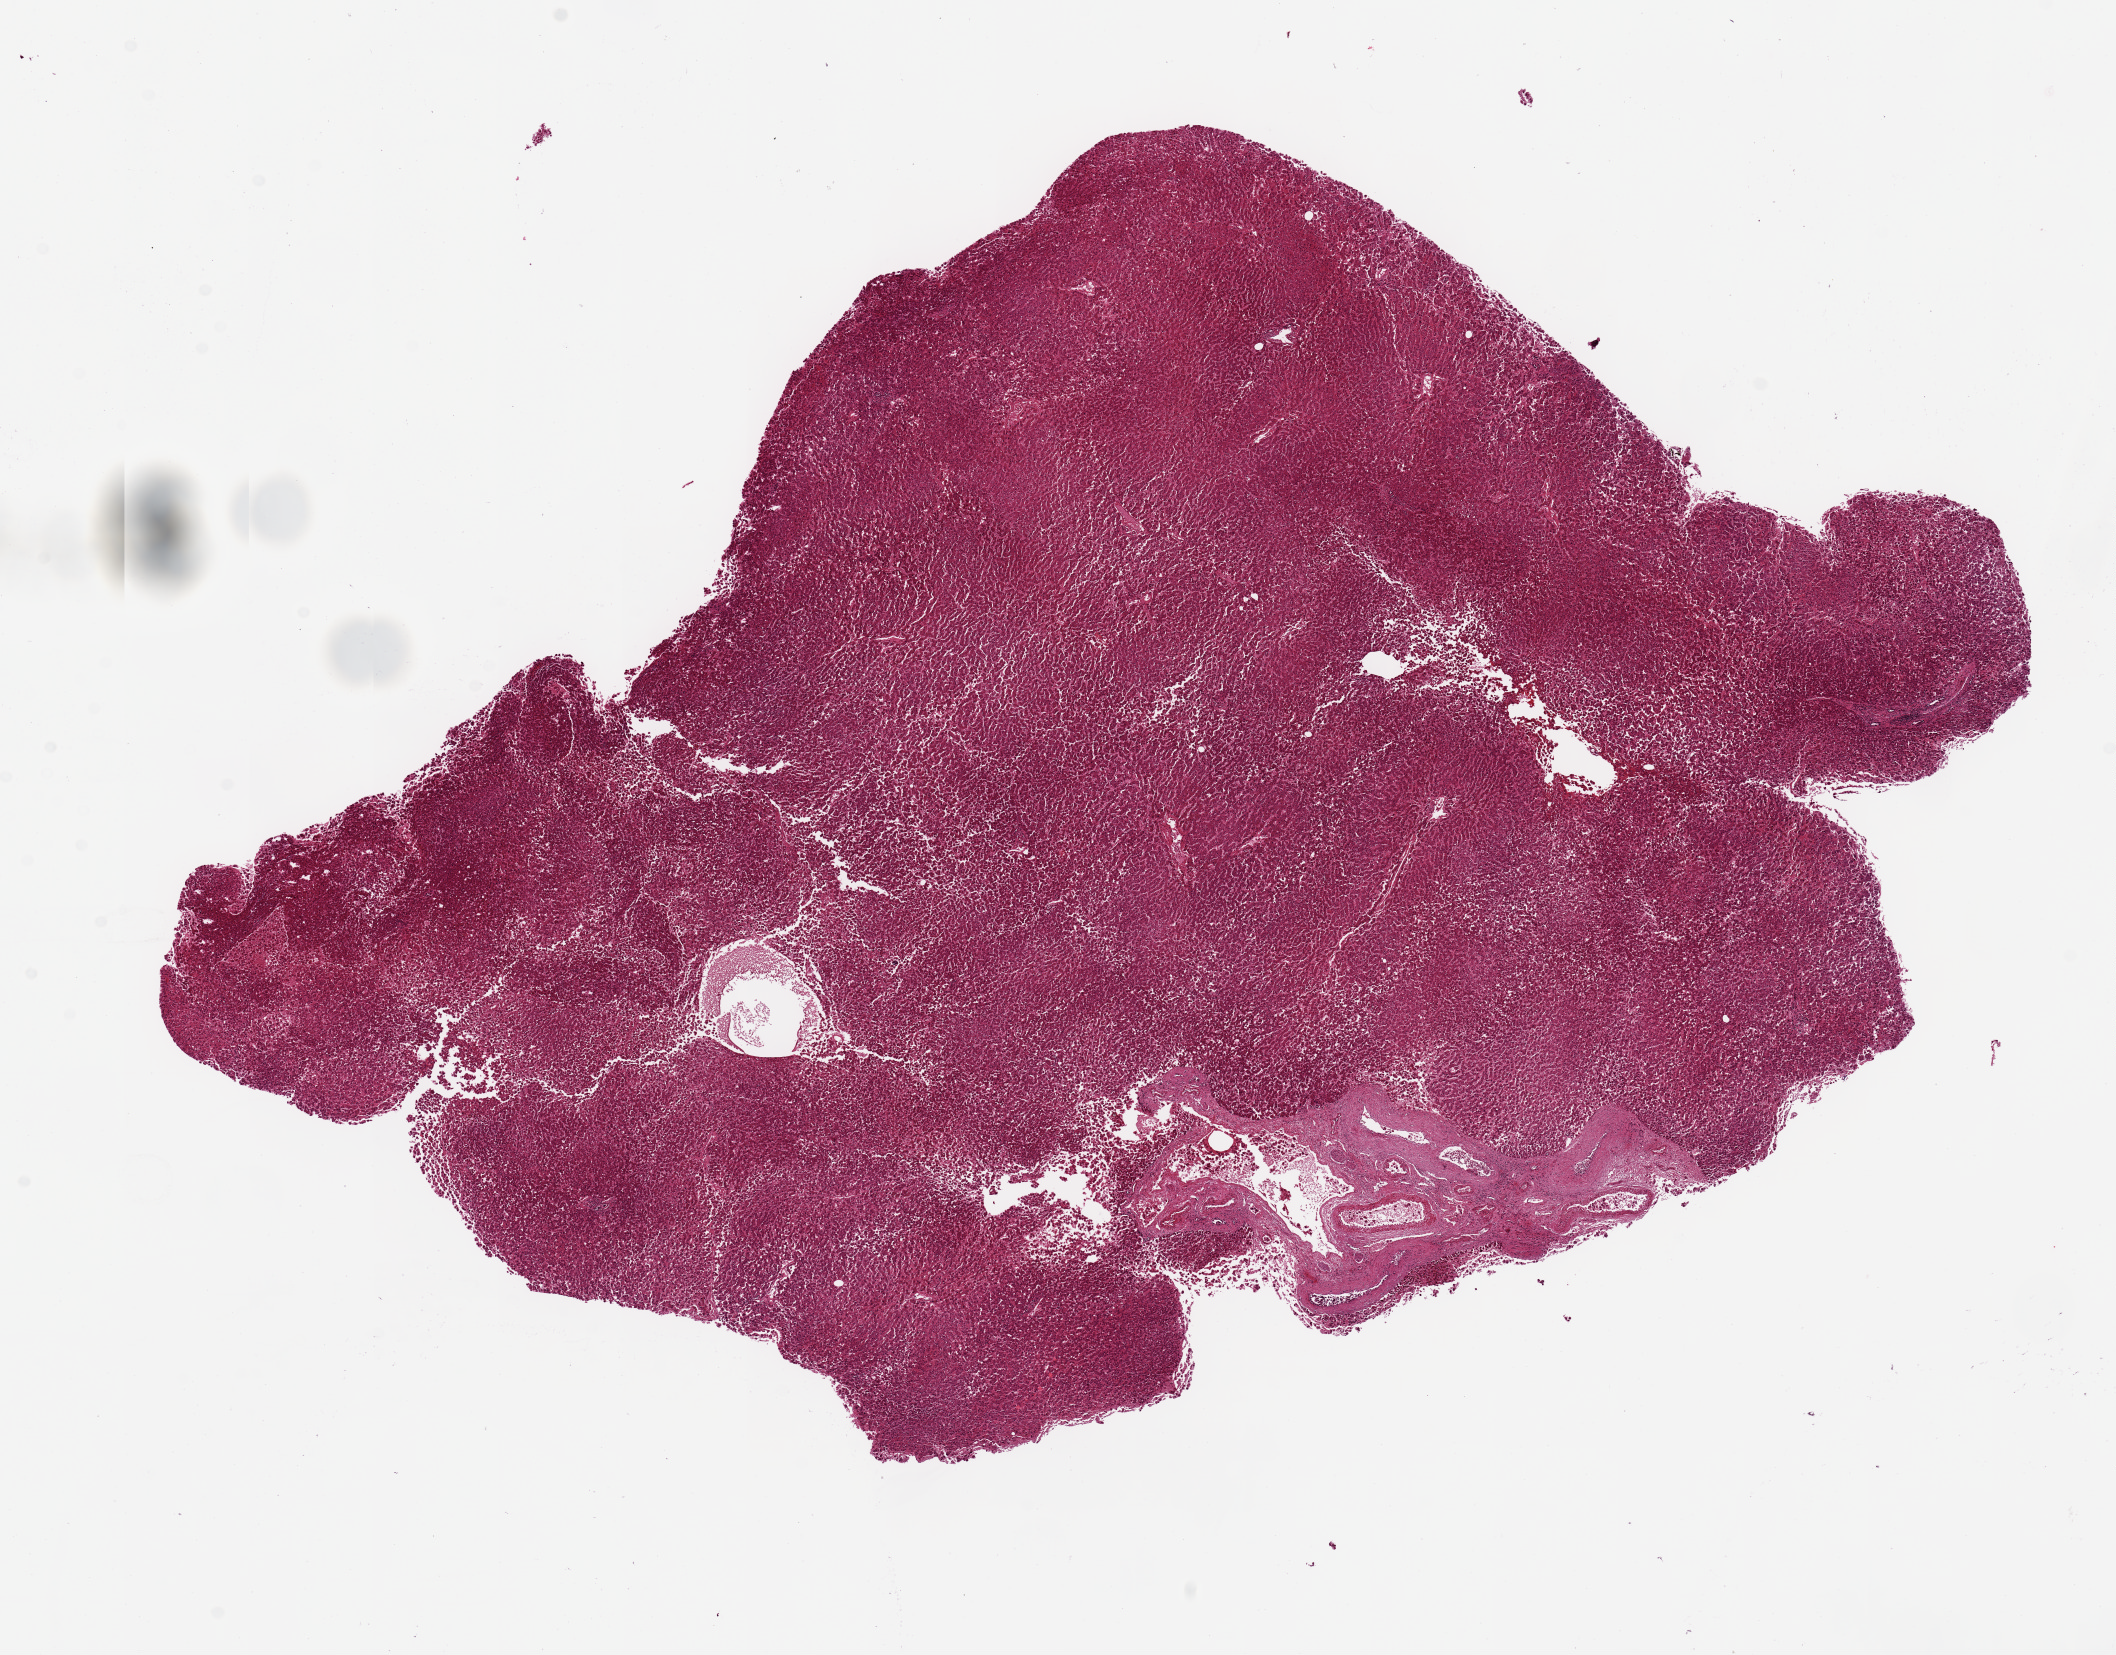
Digitized hematoxylin and eosin (H&E)-stained section, low-resolution overview of the scanned area, about 16.7 x 13.1 mm, PAXgene-fixed, paraffin-embedded tissue, sampled site (target tissue): liver, tissue donor sample. Female donor.
Review note (as recorded): 11.4x7.8. Central round hole.